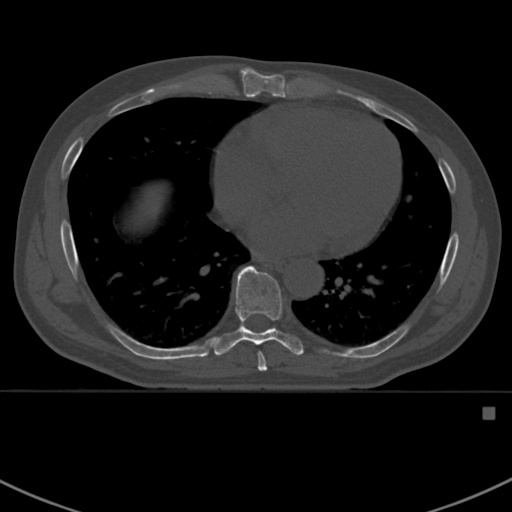
CT including the spine, one axial slice; position 401 of 412 along the scan axis; reconstruction kernel Br40s; 120 kVp; bone window (W 1800 / L 400 HU); 1.5 mm slice thickness; 512 × 512 image matrix, field of view 358 × 358 mm. Male patient, age 59 years. Case-level facts recorded for this patient, not image findings: primary cancer: prostate.
Outlined on this slice (semi-automatically segmented with operator editing):
- T7 vertebra: bounding box [x1, y1, x2, y2] px = [258, 352, 267, 371]
- T8 vertebra: [213, 266, 303, 356]